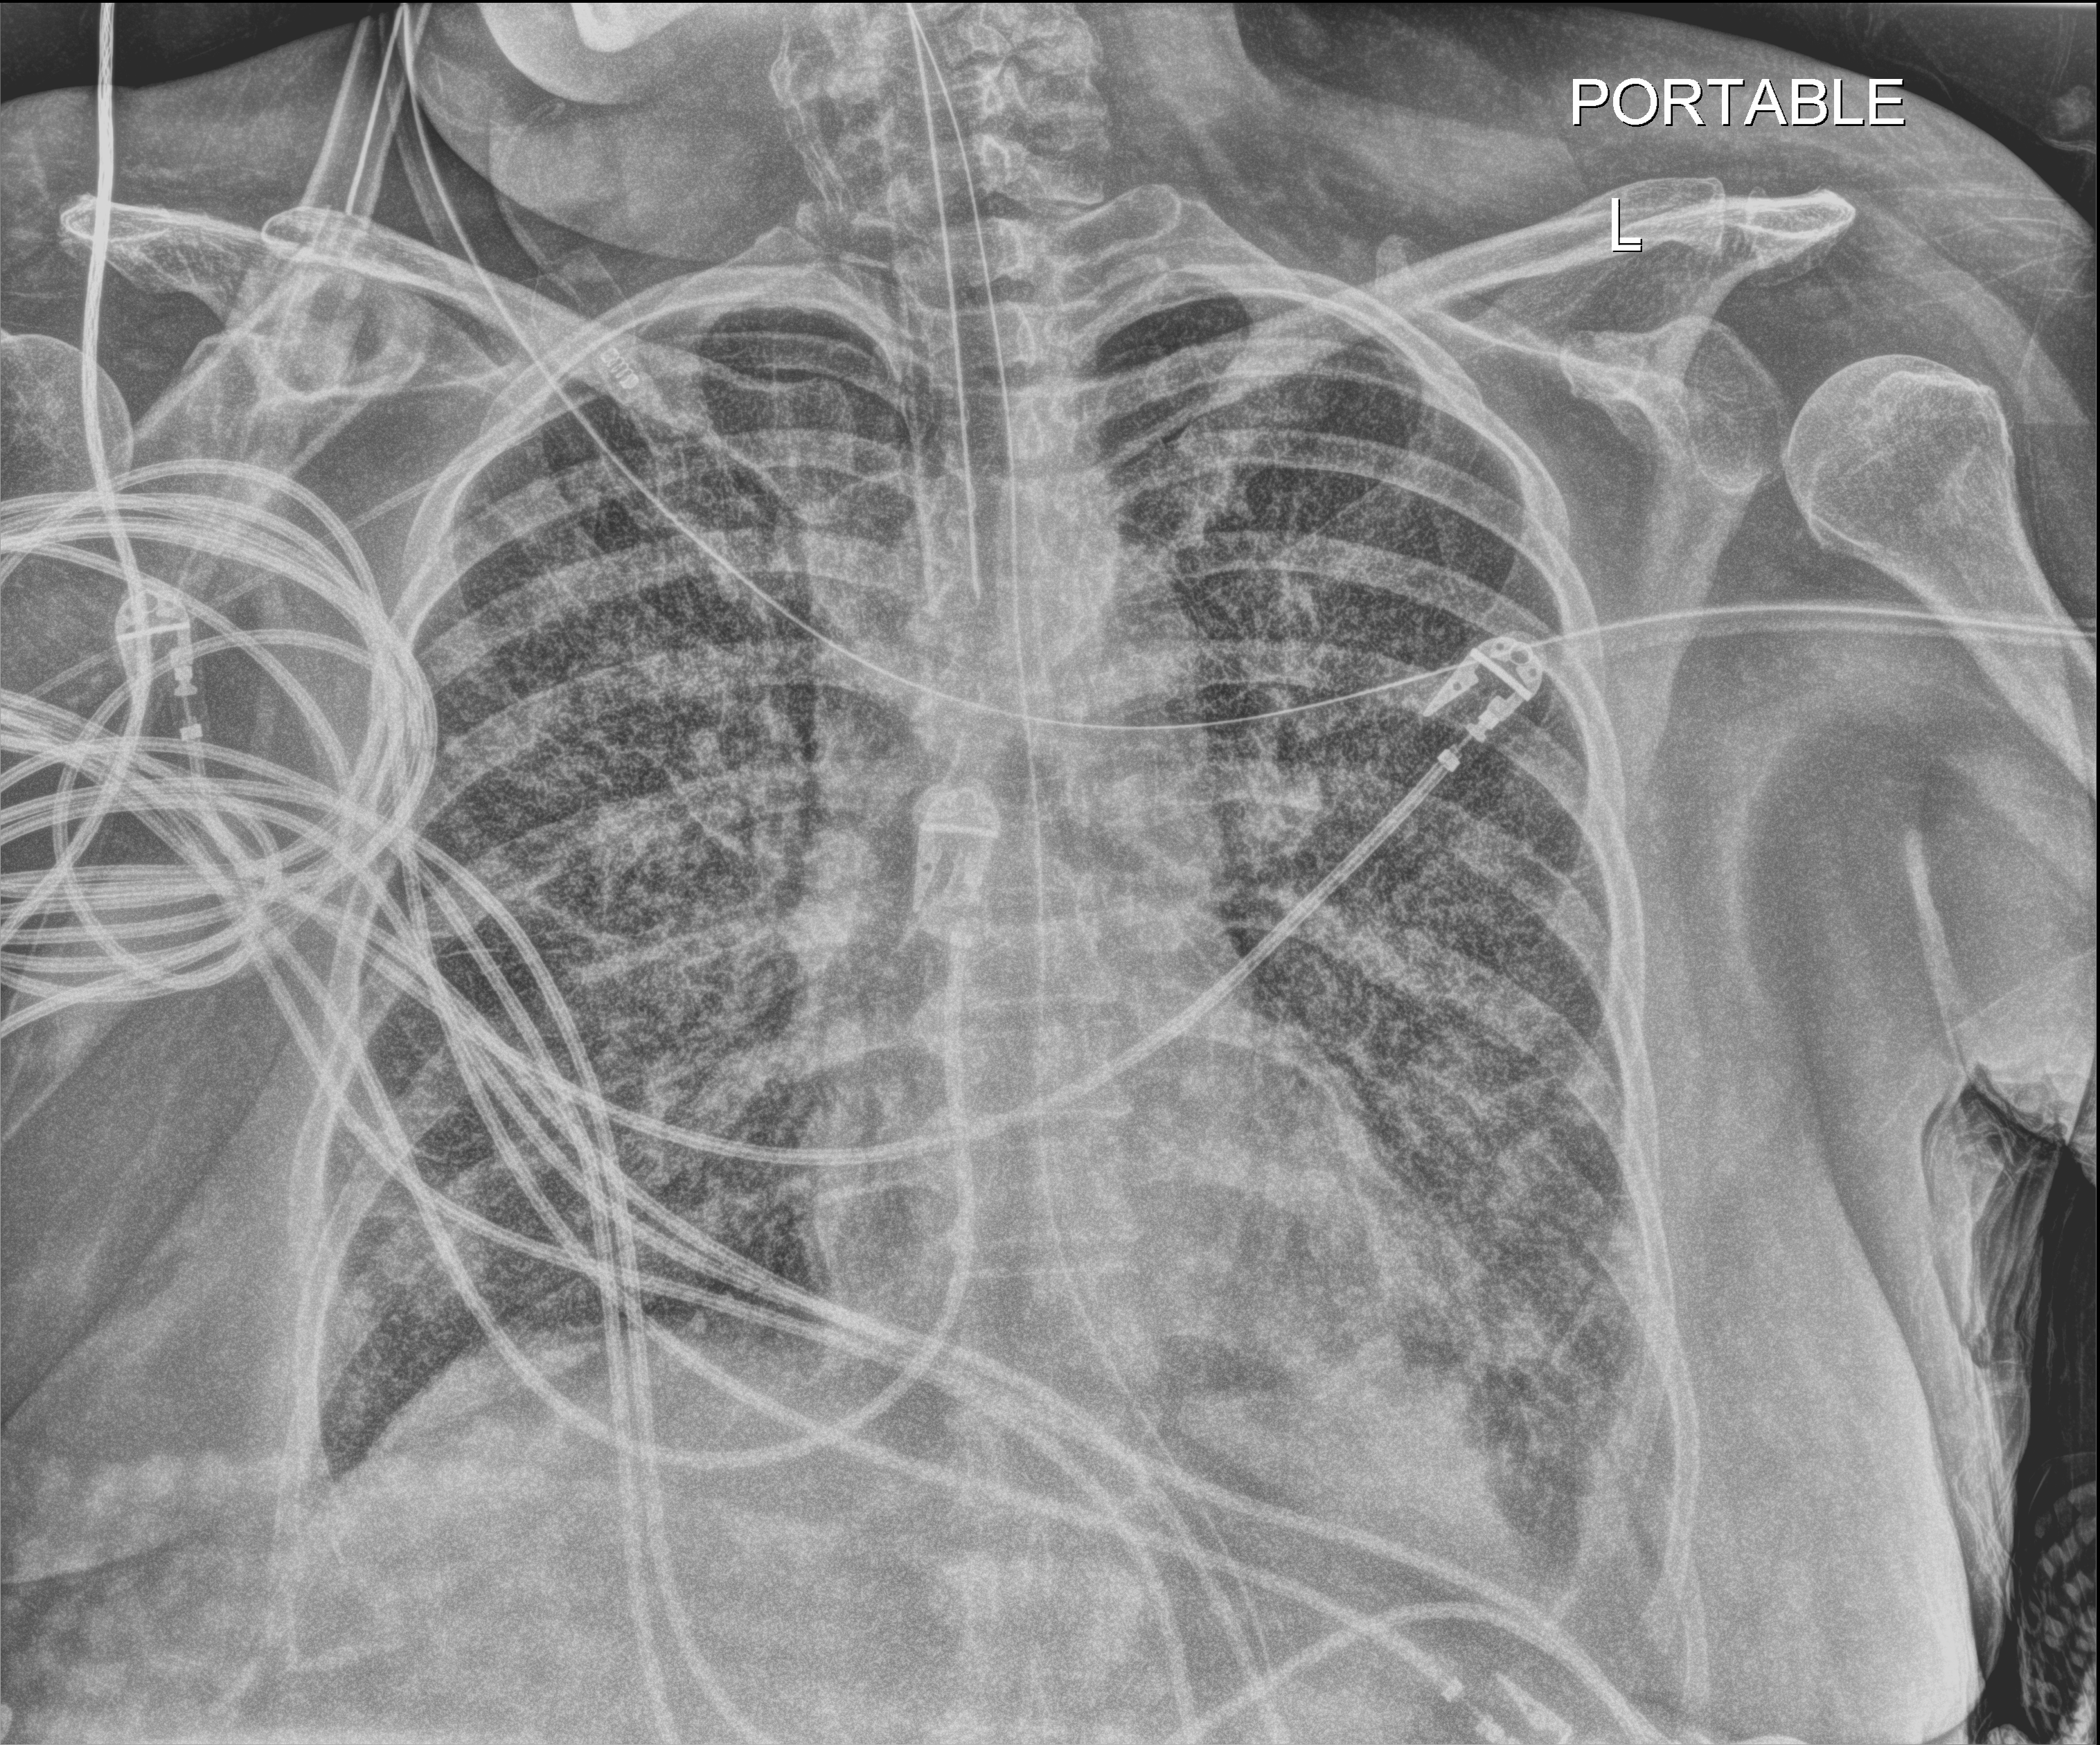
Bedside chest radiograph (digital radiography); anteroposterior (AP) projection. Patient hospitalised with COVID-19; female, aged 60–74 years.
Hospital-stay facts (about this admission, not read from this image; timing relative to this image not recorded):
- length of hospital stay: 38 days
- mechanically ventilated during this hospital stay: yes
- admitted to intensive care during this hospital stay: yes